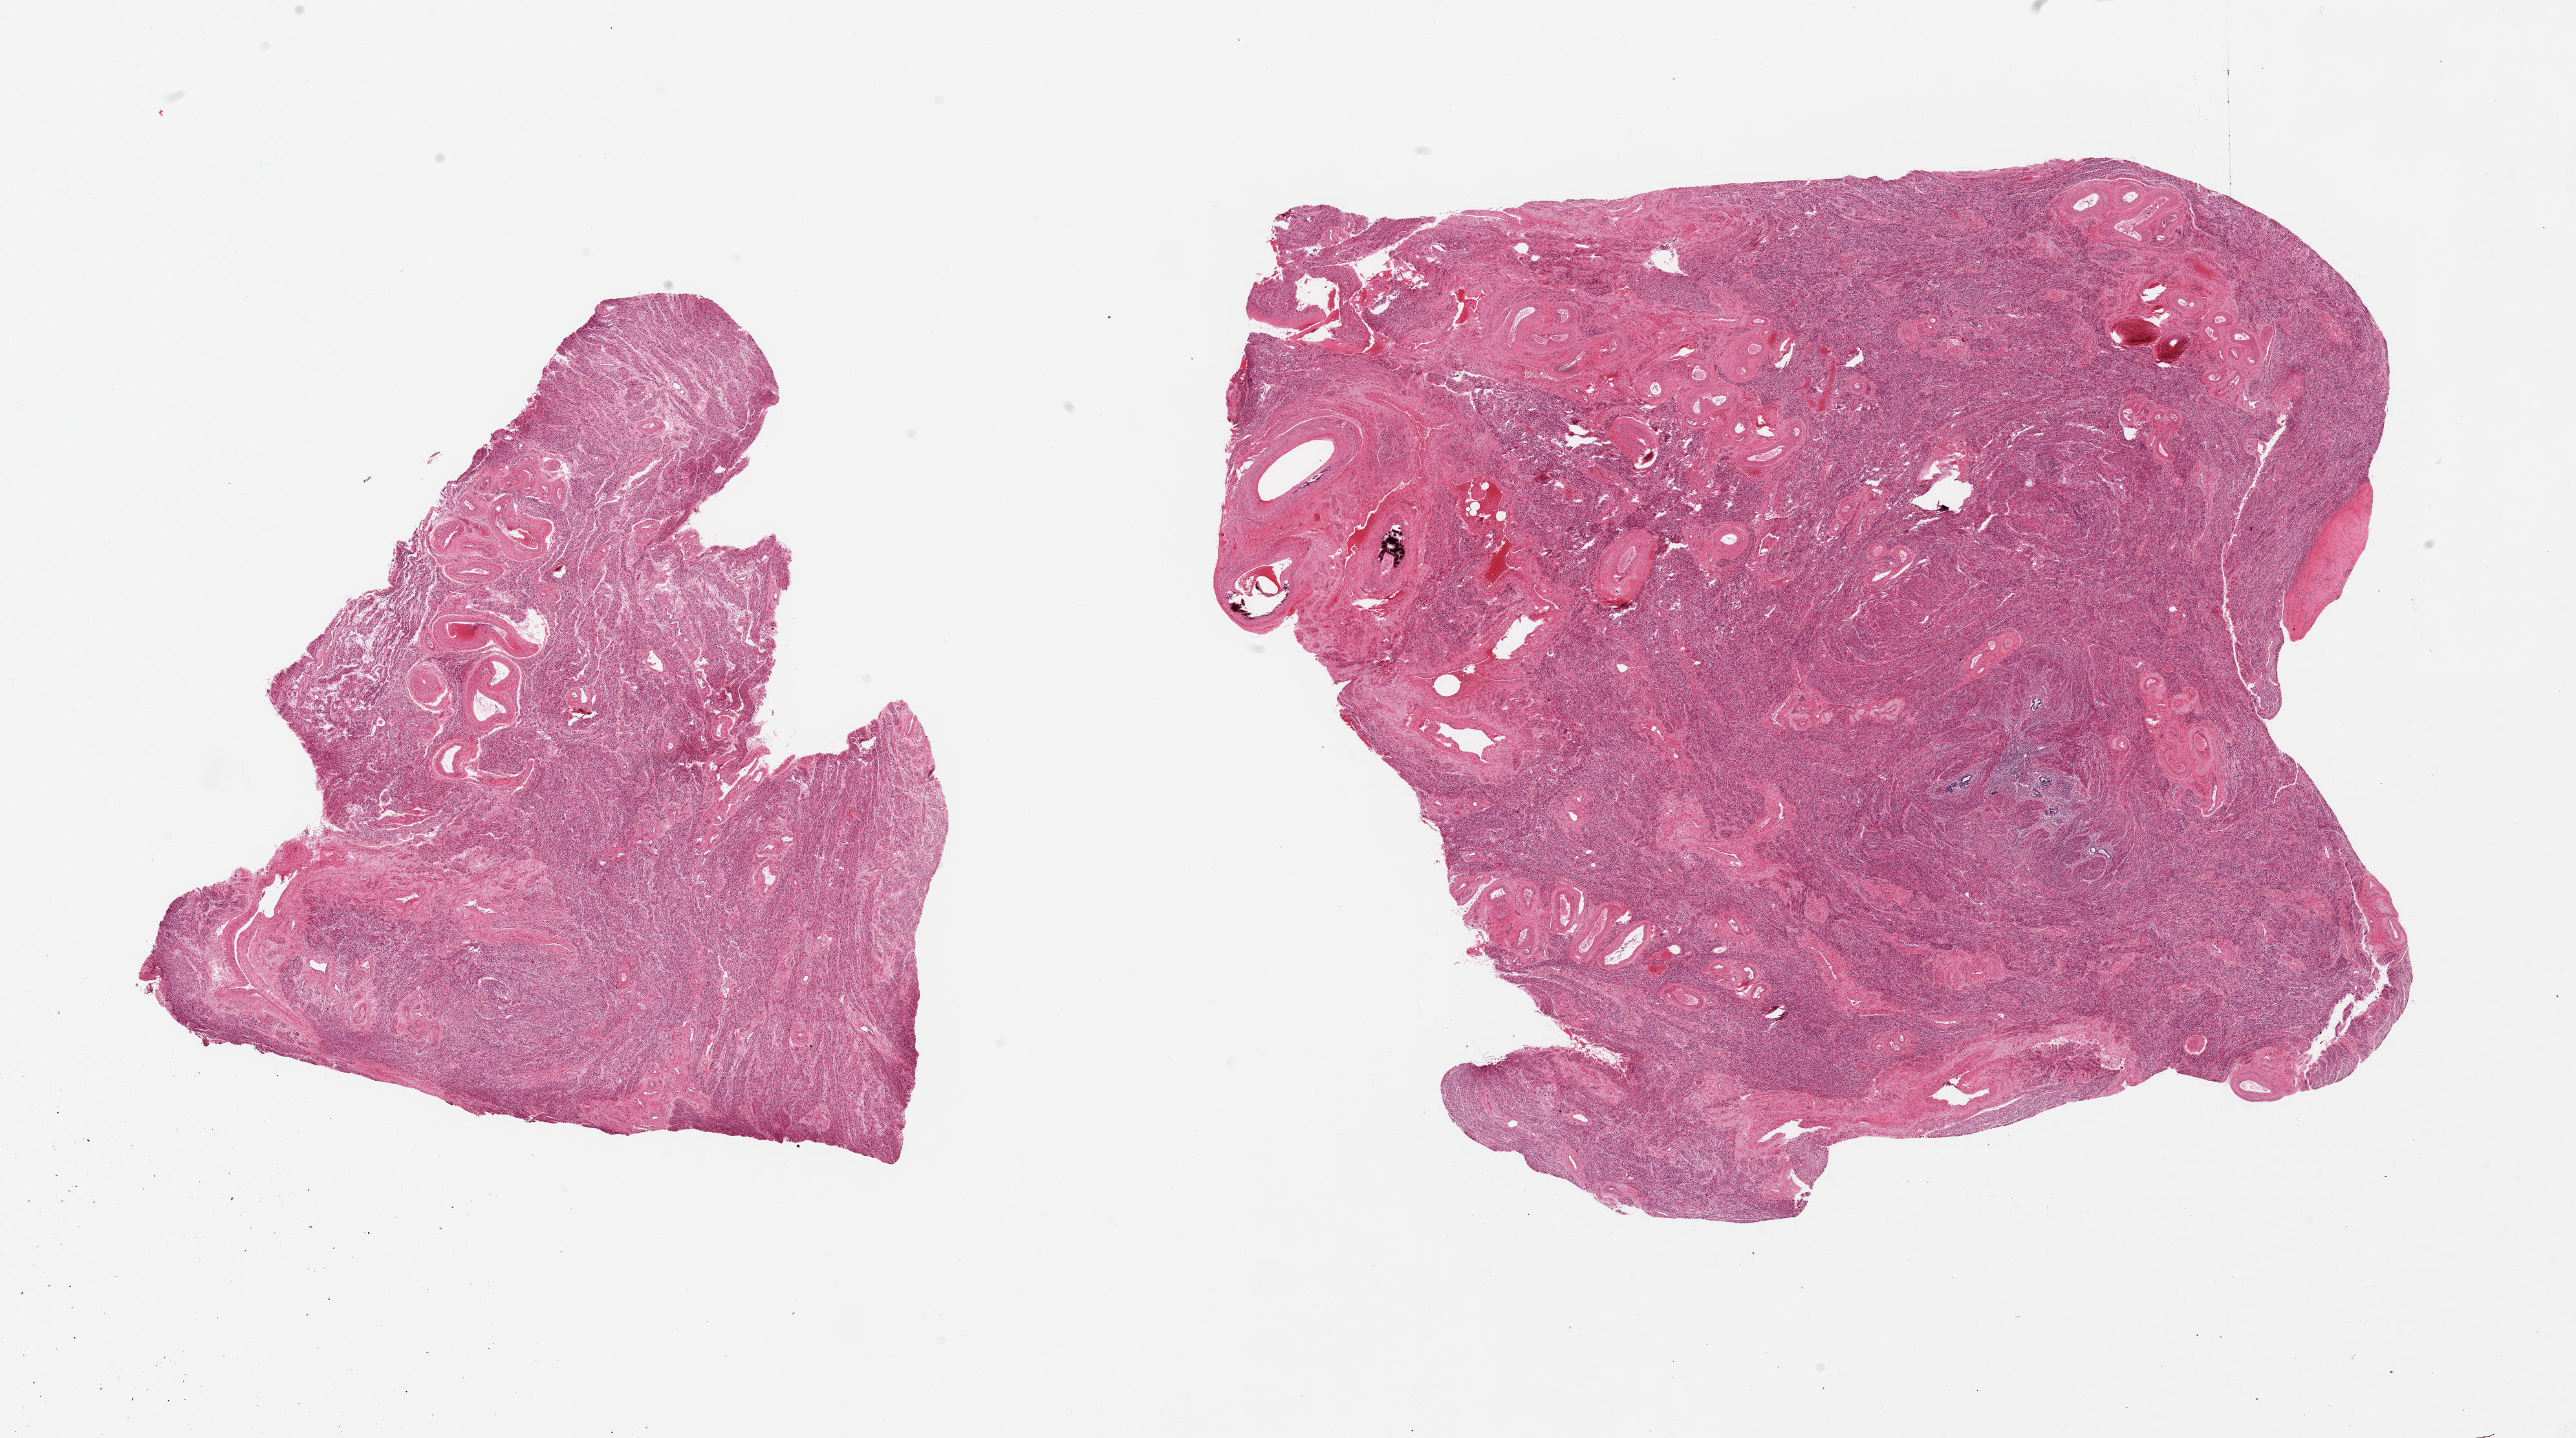
Whole-slide image, H&E stain, brightfield — shown as a low-resolution overview of the whole scanned area (about 31.5 x 17.6 mm, acquisition: 20x scan), PAXgene-fixed, paraffin-embedded tissue, sampled site (target tissue): uterus, tissue donor sample.
- pathologist's review note for this sample: 2 pieces; thick walled vessels with calcifications, myometrium and focus of adenomyosis